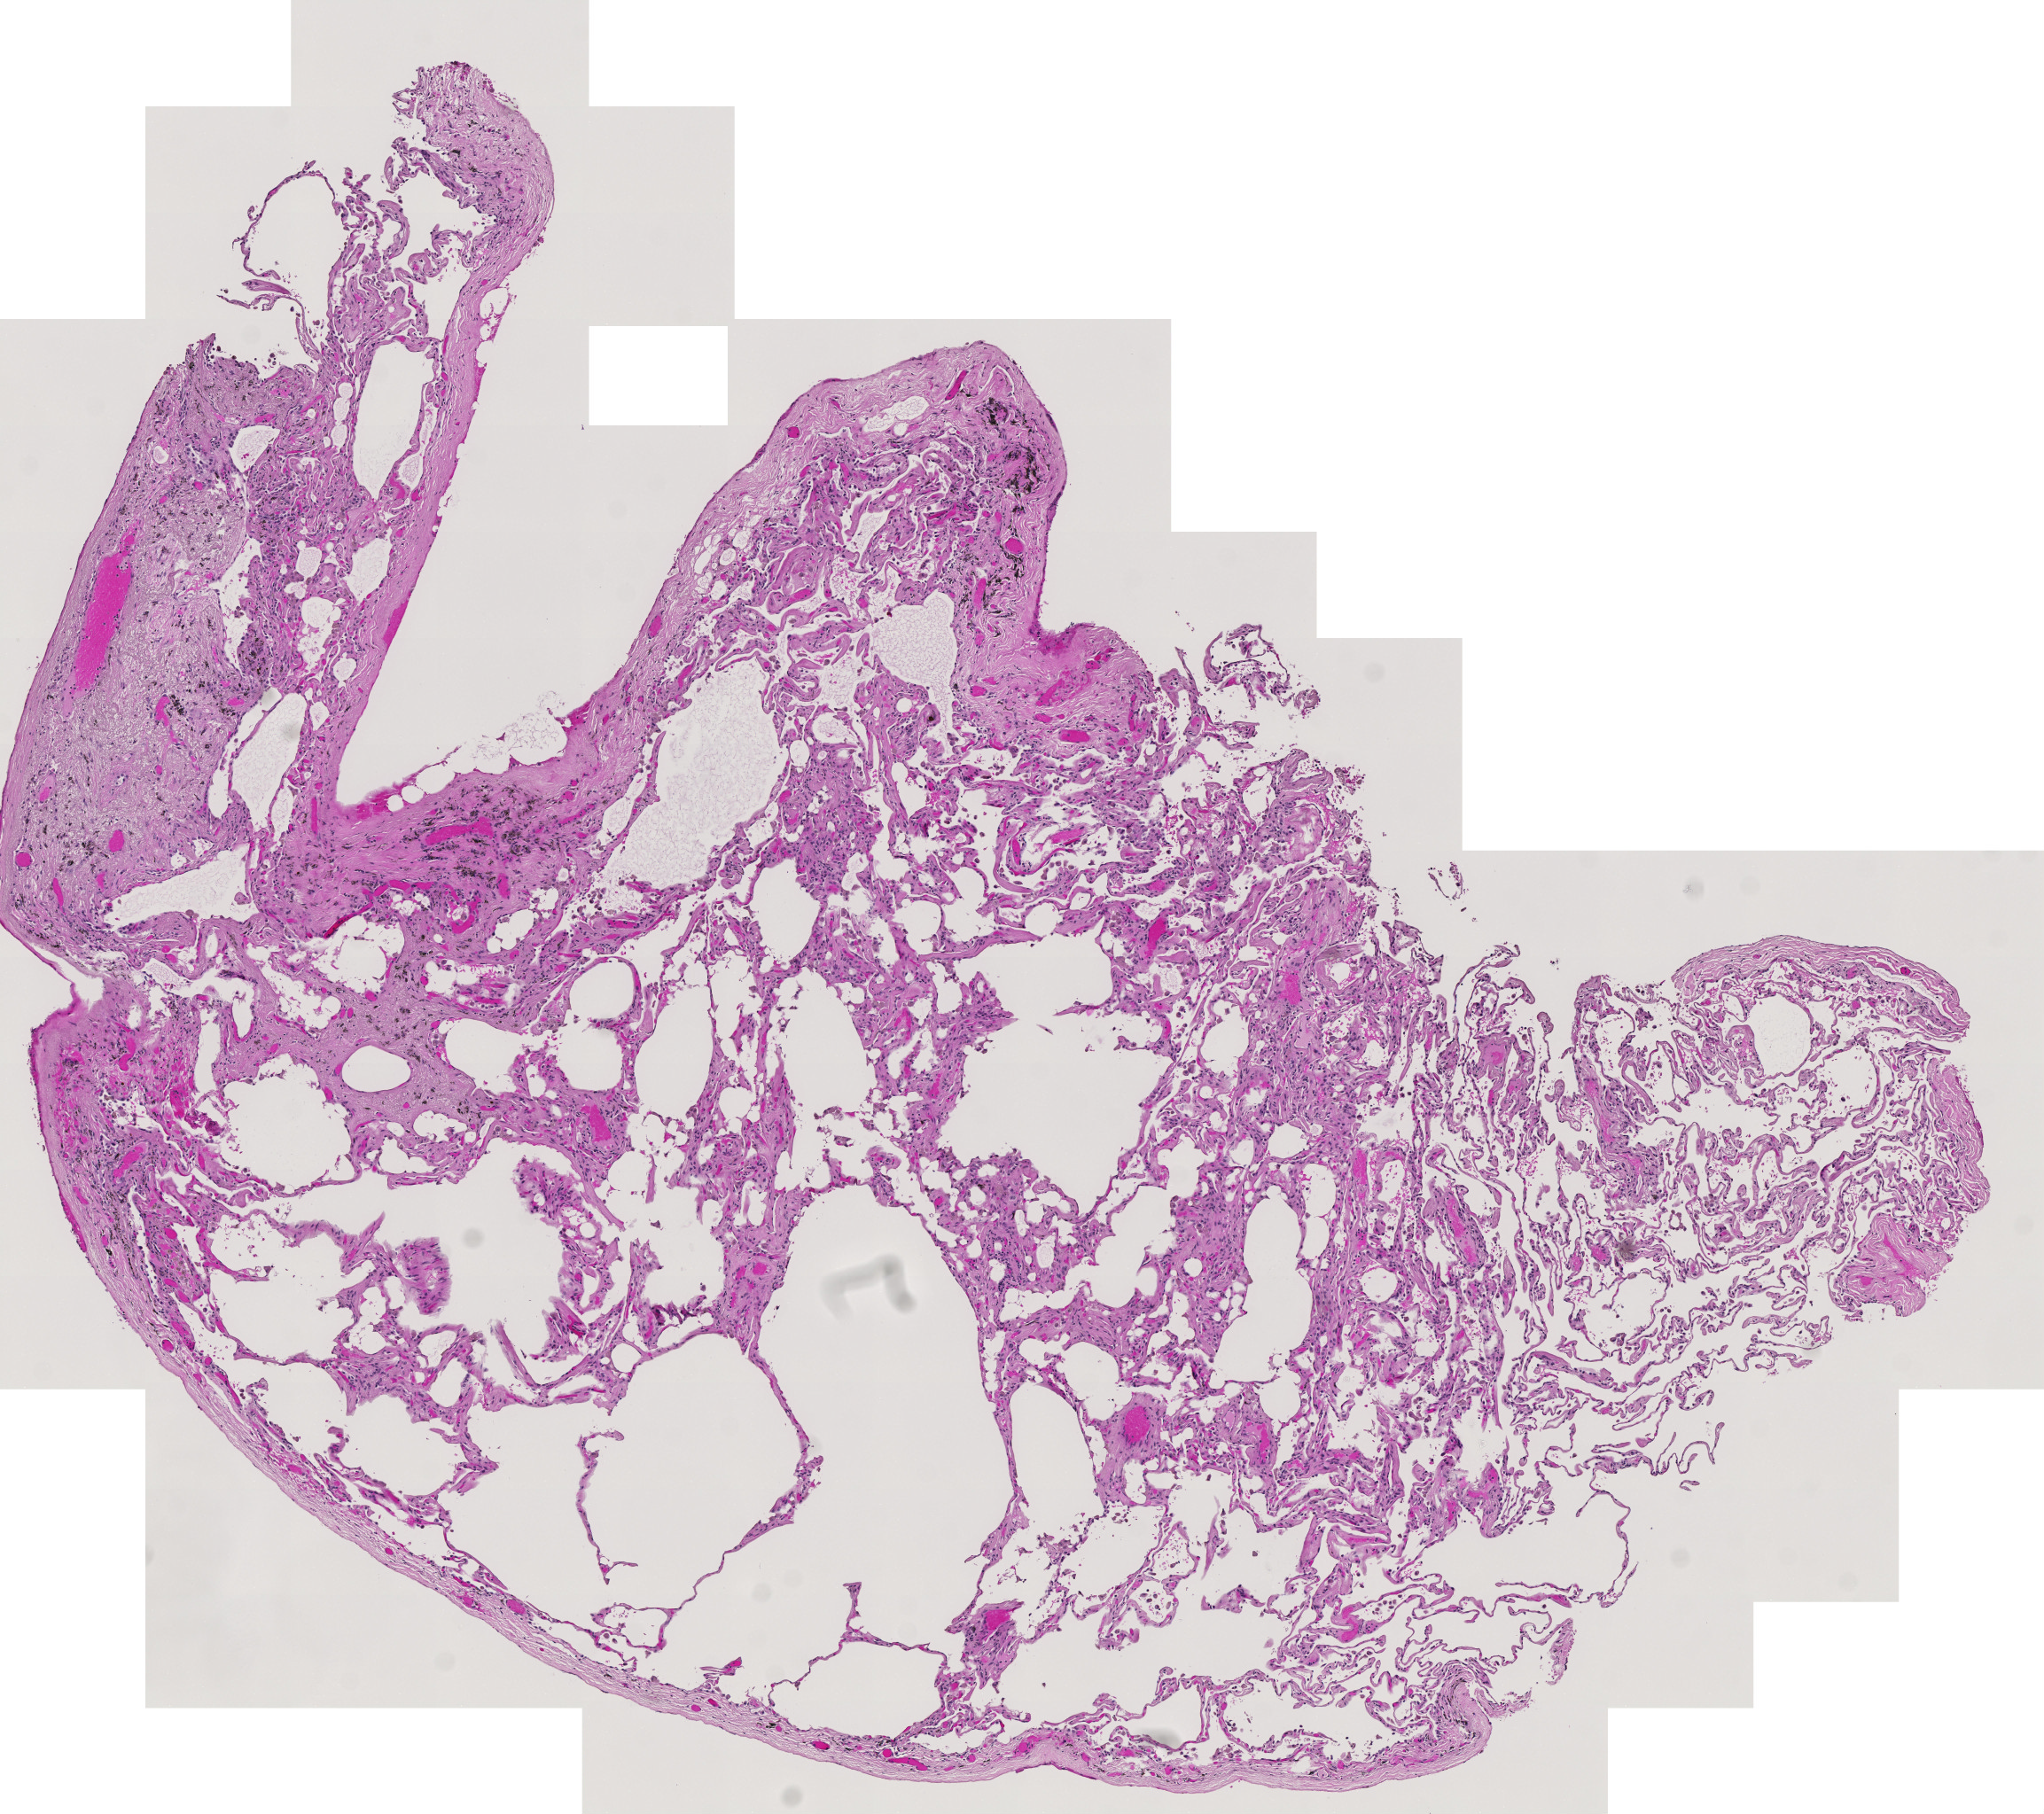
Hematoxylin and eosin (H&E) stained whole-slide image, a low-resolution overview of the entire scanned area, about 6.0 x 5.3 mm. Lung, normal (non-tumour) tissue. 68-year-old female patient.
This section: normal (non-tumour) tissue from the same patient. Patient diagnosis: Adenocarcinoma, NOS.